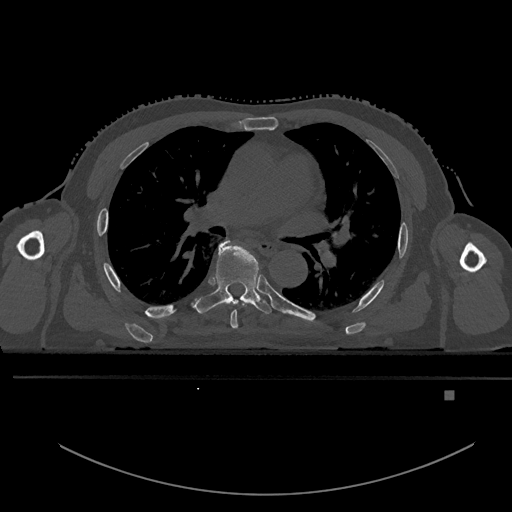
CT including the spine, one axial slice; slice 323 of 969 in the series (ordered by position); bone window (W 1800 / L 400 HU); 0.5 mm slice thickness; 512 × 512 image matrix, field of view 456 × 456 mm. Male patient, age 82 years. From the clinical record (not read from this slice): primary cancer: prostate; vertebrae with lytic lesions (as recorded): T11, T9, T8, T2.
Outlined on this slice (semi-automatic segmentation, software-assisted and operator-edited):
- T5 vertebra: bounding box <228,242,238,329> (left, top, right, bottom; pixels)
- T6 vertebra: <192,238,273,314>